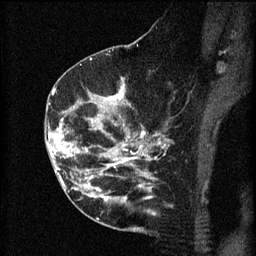
Breast MRI (dynamic contrast-enhanced), one sagittal slice; position 32 of 60 along the scan axis; 3 images stored at this slice position (order not interpretable as contrast timing); 1.5 T; TE 4.2 ms, TR 8.2 ms; 256 × 256 image matrix, field of view 180 × 180 mm. Female patient, age 49 years.
Outlined on this slice (semi-automatic segmentation, software-assisted and operator-edited):
- analysis volume of interest (the breast-tissue region the enhancement analysis was run in; not a lesion): bounding box [x1, y1, x2, y2] px = [45, 126, 105, 177]
- tumour enhancement mask (voxels above the 70 % enhancement threshold inside the analysis volume of interest): [47, 126, 105, 175]